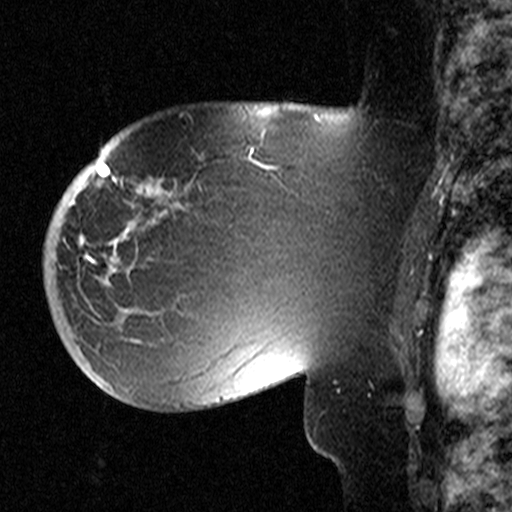
Breast MRI (dynamic contrast-enhanced), one sagittal slice. Slice 31 of 44 in the series (ordered by position). Dynamic contrast-enhanced study with each time point stored as its own series, time point 2 of 3 at this slice position (early post-contrast, ordered by acquisition time). 1.5 T. TE 4.5 ms, TR 11 ms. 512 × 512 image matrix, field of view 200 × 200 mm. Patient: female, 53 years. From the clinical record (not read from this slice): setting: breast cancer imaged before/during neoadjuvant chemotherapy; receptor status: HR-positive, HER2-negative.
Structures marked on this image (semi-automatic segmentation, software-assisted and operator-edited):
- analysis volume of interest (the breast-tissue region the enhancement analysis was run in; not a lesion): box from (x=58, y=154) to (x=311, y=367) px
- tumour enhancement mask (voxels above the 90 % enhancement threshold inside the analysis volume of interest): (x=80, y=178)–(x=169, y=265)